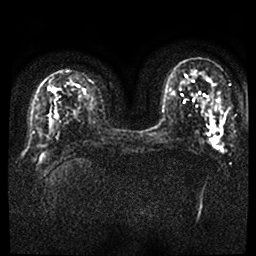
Breast MRI, one axial slice. Position 18 of 50 along the scan axis. Diffusion-weighted series; image 2 of 4 stored at this slice position (different b-values; order by instance number). 1.5 T. 256 × 256 image matrix, field of view 340 × 340 mm. Female patient.
Annotated regions visible in this slice (outlined manually by an expert reader):
- tumour on diffusion-weighted imaging: bounding box [x1, y1, x2, y2] px = [212, 125, 224, 152]